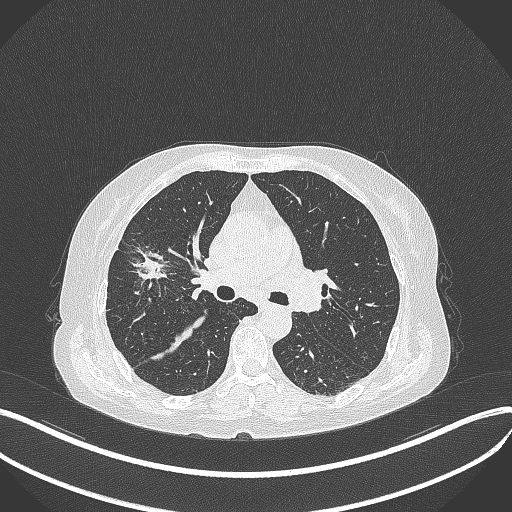
Chest CT, one axial slice; slice 241 of 429 in the series (ordered by position); reconstruction kernel B70f; 120 kVp; lung window (W 1500 / L -600 HU); 1 mm slice thickness; 512 × 512 image matrix, field of view 400 × 400 mm. Female patient, age 69 years. From the clinical record (not read from this slice): clinical TNM (as recorded): T1b N3 M0.
Outlined on this slice (bounding box drawn by a radiologist):
- lung tumour (recorded histology: small cell carcinoma): bounding box [x1, y1, x2, y2] px = [119, 239, 173, 289]